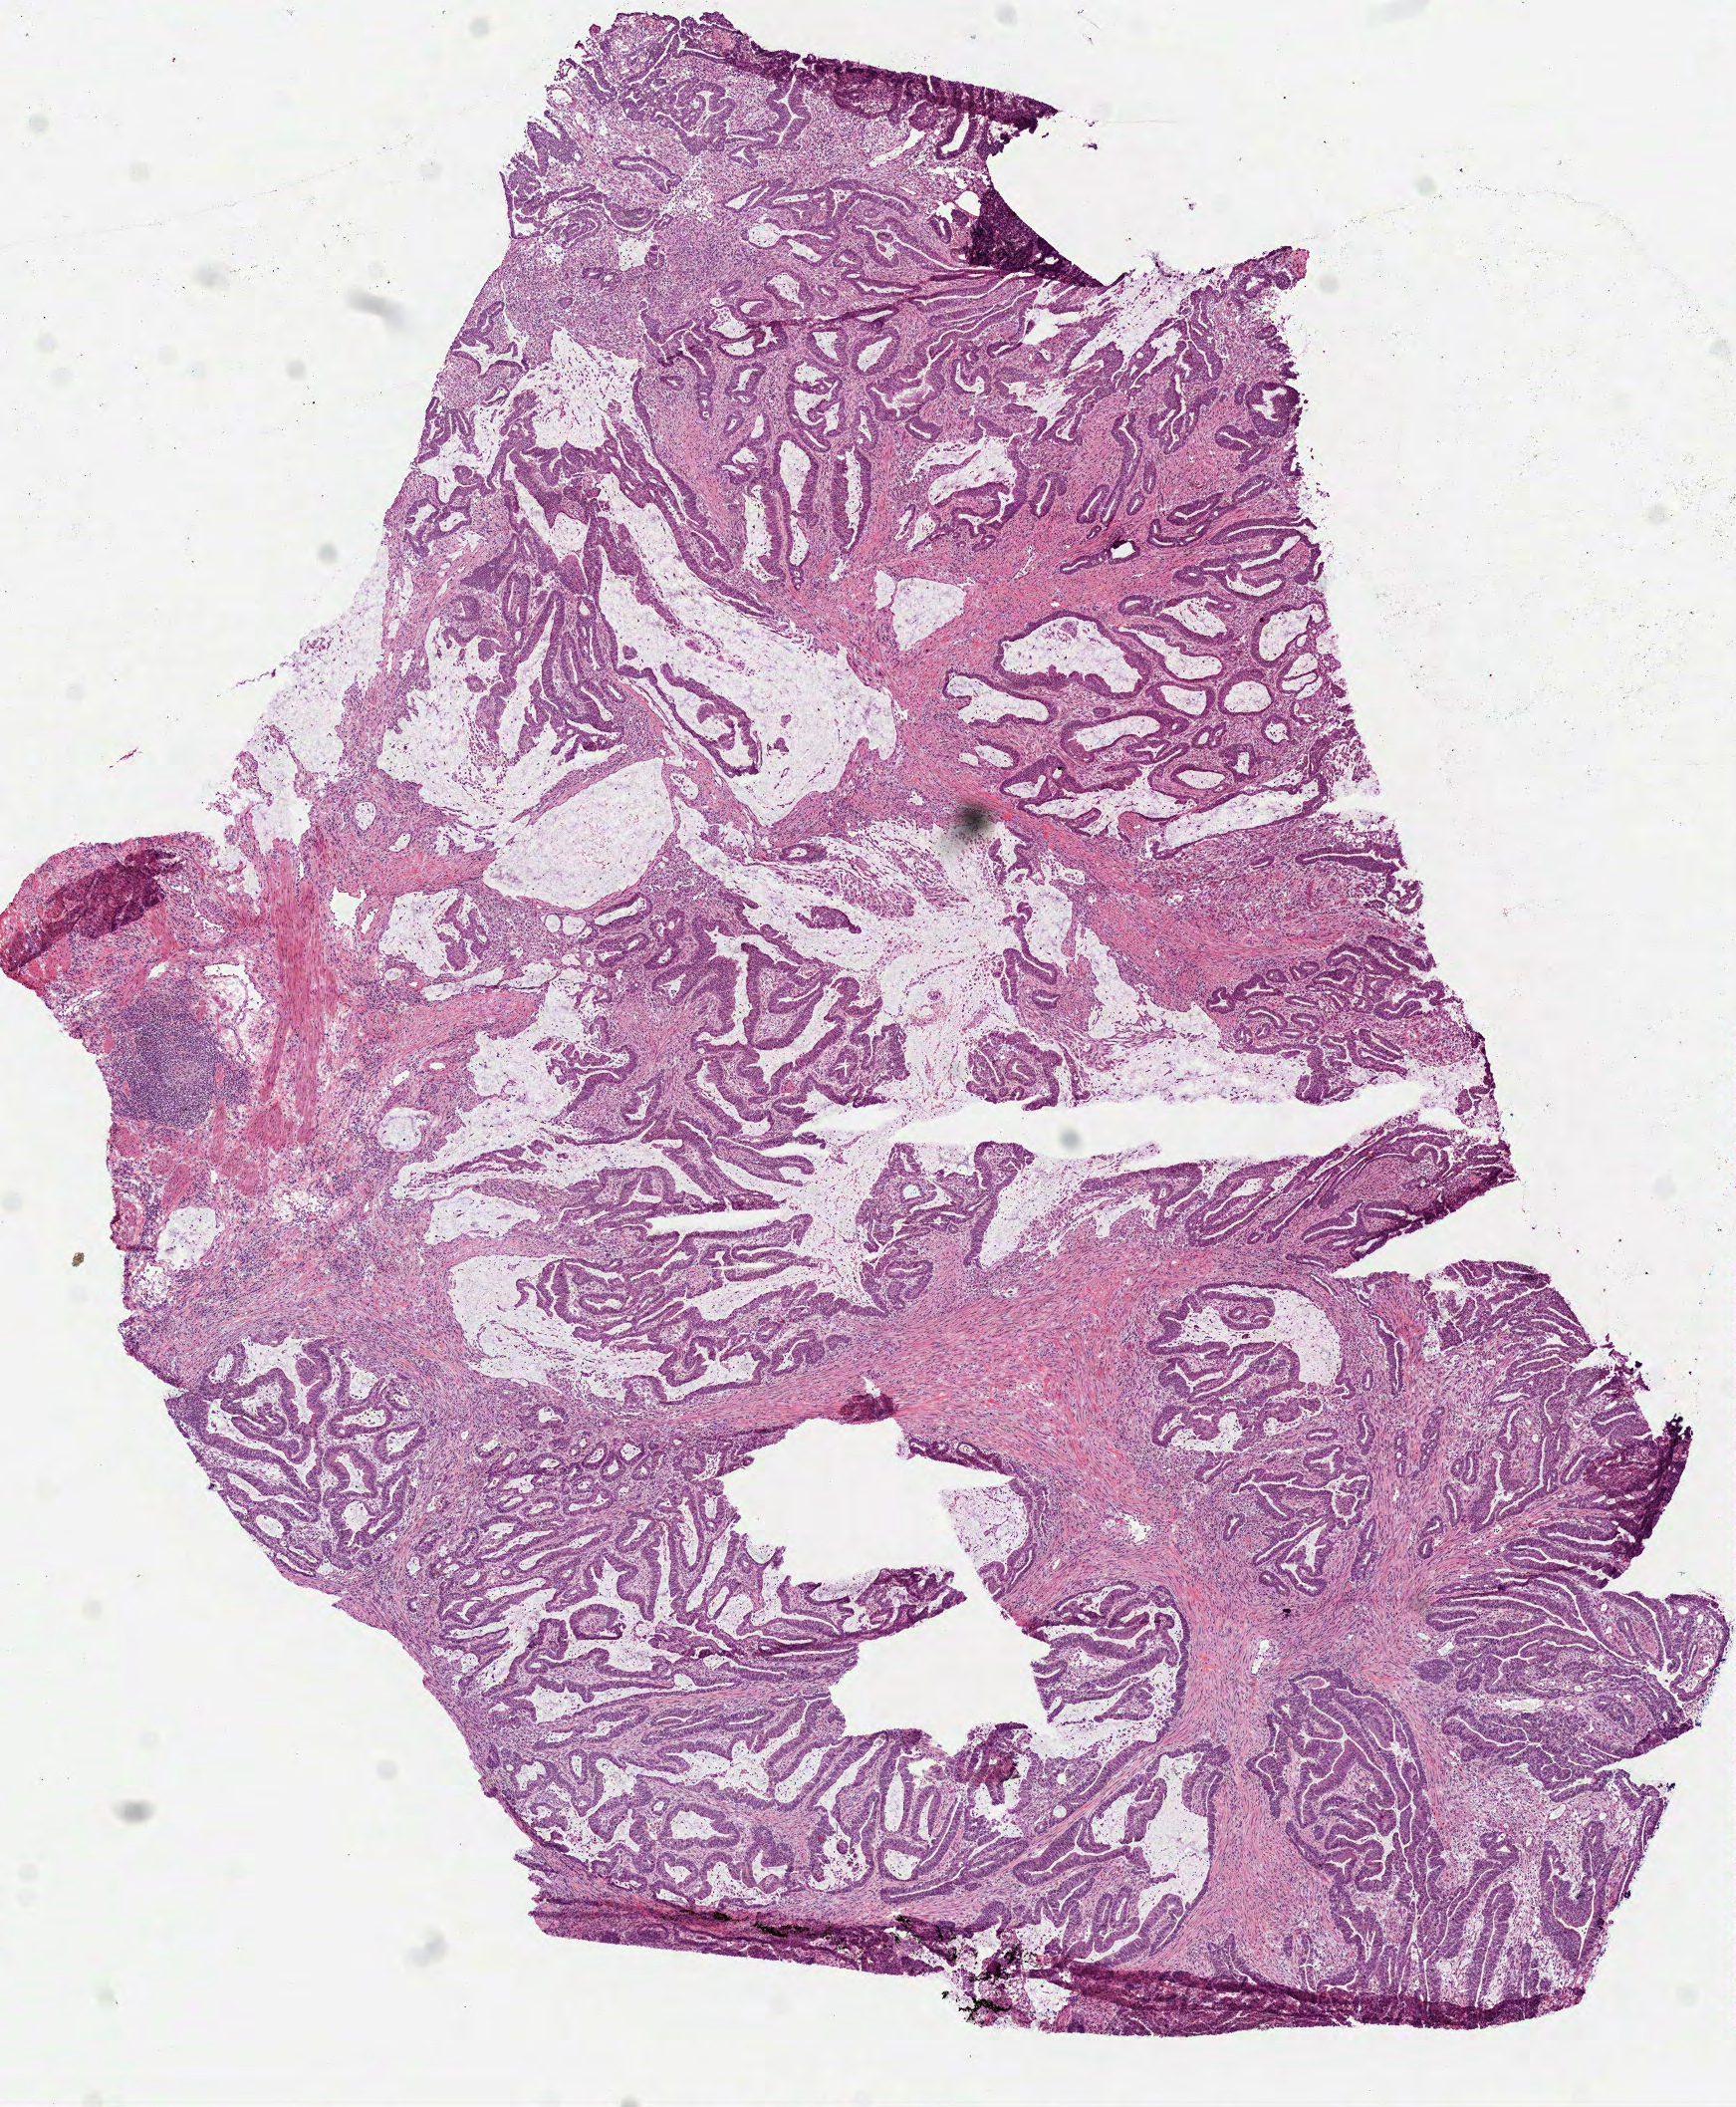
Whole-slide histology image, H&E — low-resolution overview of the scanned area, about 7.0 x 8.5 mm (acquisition: 40x scan); frozen section from the bottom of the tissue portion; colon, primary tumour sample. Patient: male, age at initial diagnosis 82 years. Composition of this section per pathologist review: tumour cells 100%, tumour nuclei 71%, normal cells 0%, stromal cells 0%, necrosis 0%. Infiltration values recorded for this section: lymphocyte infiltration 15%, monocyte infiltration 1%, neutrophil infiltration 2%.
* TNM: T2 N0 M0
* pathologic diagnosis: Adenocarcinoma, NOS
* AJCC pathologic stage: I